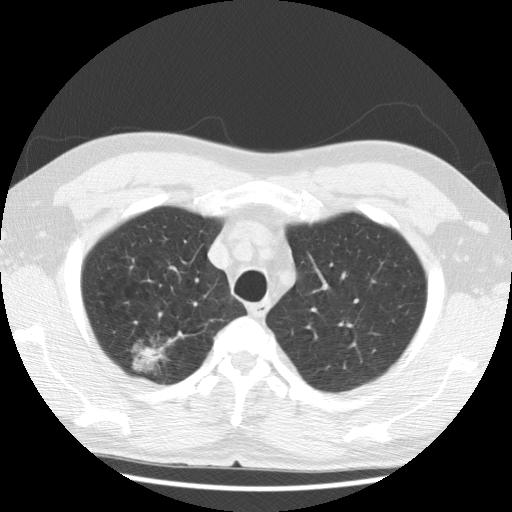
Low-dose screening chest CT, one axial slice. Position 97 of 122 along the scan axis. Reconstruction kernel STANDARD. 120 kVp. Lung window (W 1500 / L -600 HU). 2.5 mm slice thickness. 512 × 512 image matrix, field of view 350 × 350 mm.
Outlined on this slice (outlined manually by an expert reader):
- lesion 1 (tumor, upper lobe of right lung): bounding box (x1, y1, x2, y2) in pixels: (136, 348, 158, 371)